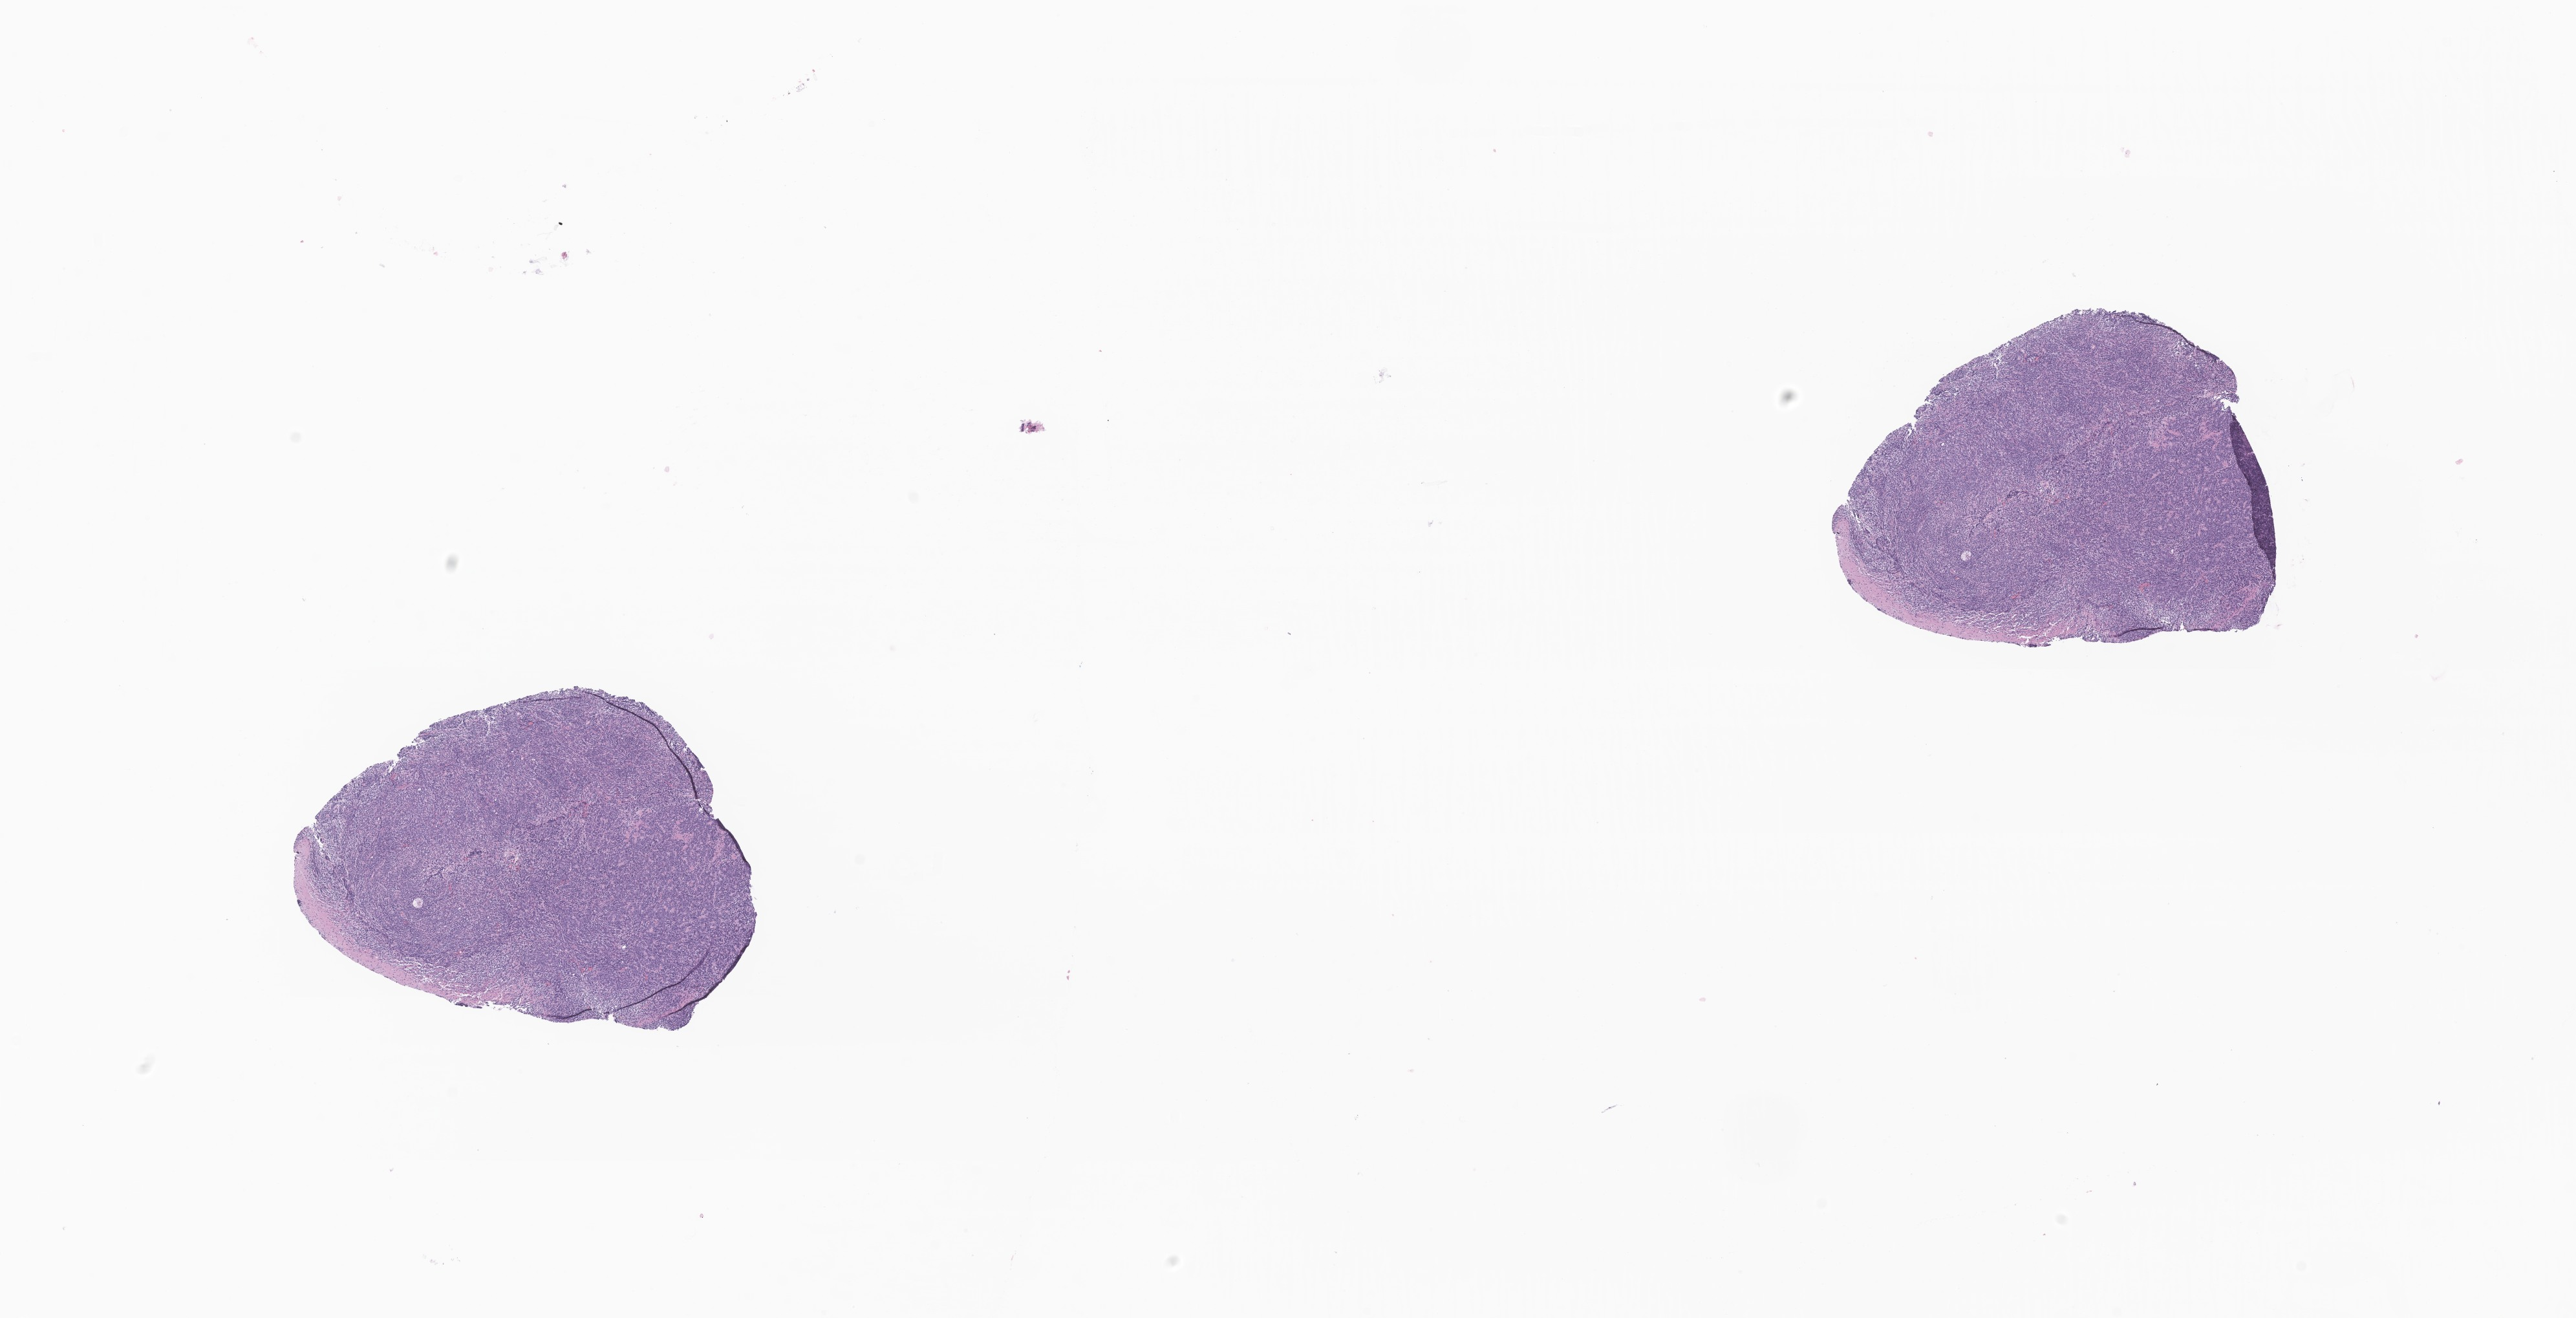
Whole-slide image, haematoxylin and eosin stain of tumor tissue from the brain, low-resolution overview of the scanned area, about 16.8 x 8.6 mm, formalin-fixed paraffin-embedded section. Patient: male, age 182 months (15 years 2 months).
Diagnosis (ICD-O-3 morphology term): Medulloblastoma, NOS.